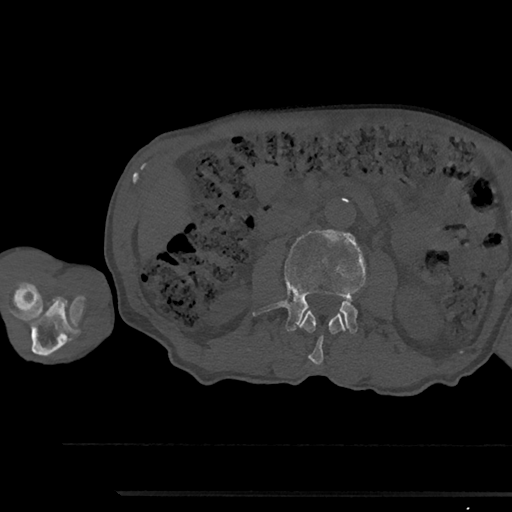
CT including the spine, one axial slice; position 520 of 797 along the scan axis; 120 kVp; bone window (W 1800 / L 400 HU); 0.5 mm slice thickness; 512 × 512 image matrix, field of view 367 × 367 mm. Patient: male, 79 years. Case-level facts recorded for this patient, not image findings: primary cancer: prostate.
Annotated regions visible in this slice (semi-automatically segmented with operator editing):
- L2 vertebra: bounding box <299,310,346,365> (left, top, right, bottom; pixels)
- L3 vertebra: <253,230,367,333>